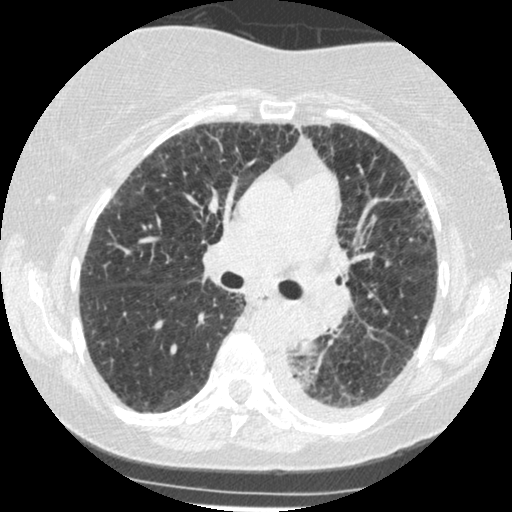
Low-dose screening chest CT, one axial slice; position 158 of 341 along the scan axis; reconstruction kernel STANDARD; lung window (W 1500 / L -600 HU); 1.25 mm slice thickness; 512 × 512 image matrix.
Structures marked on this image (manually delineated by an expert):
- lesion 1 (tumor, lower lobe of left lung): bounding box (x1, y1, x2, y2) in pixels: (291, 306, 325, 353)